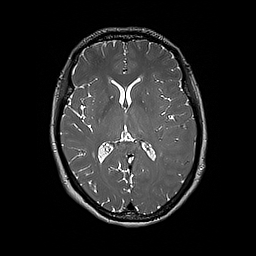
Brain MRI from a brain-tumour surgery series, one axial slice. Slice 100 of 192 in the series (ordered by position). 256 × 256 image matrix, field of view 250 × 250 mm. Case-level facts recorded for this patient, not image findings: histopathology: Glioblastoma; WHO grade: 4; IDH mutation: no; tumour location: Left Frontal.
Outlined on this slice (manually delineated by an expert):
- tumour: box from (x=178, y=164) to (x=187, y=167) px